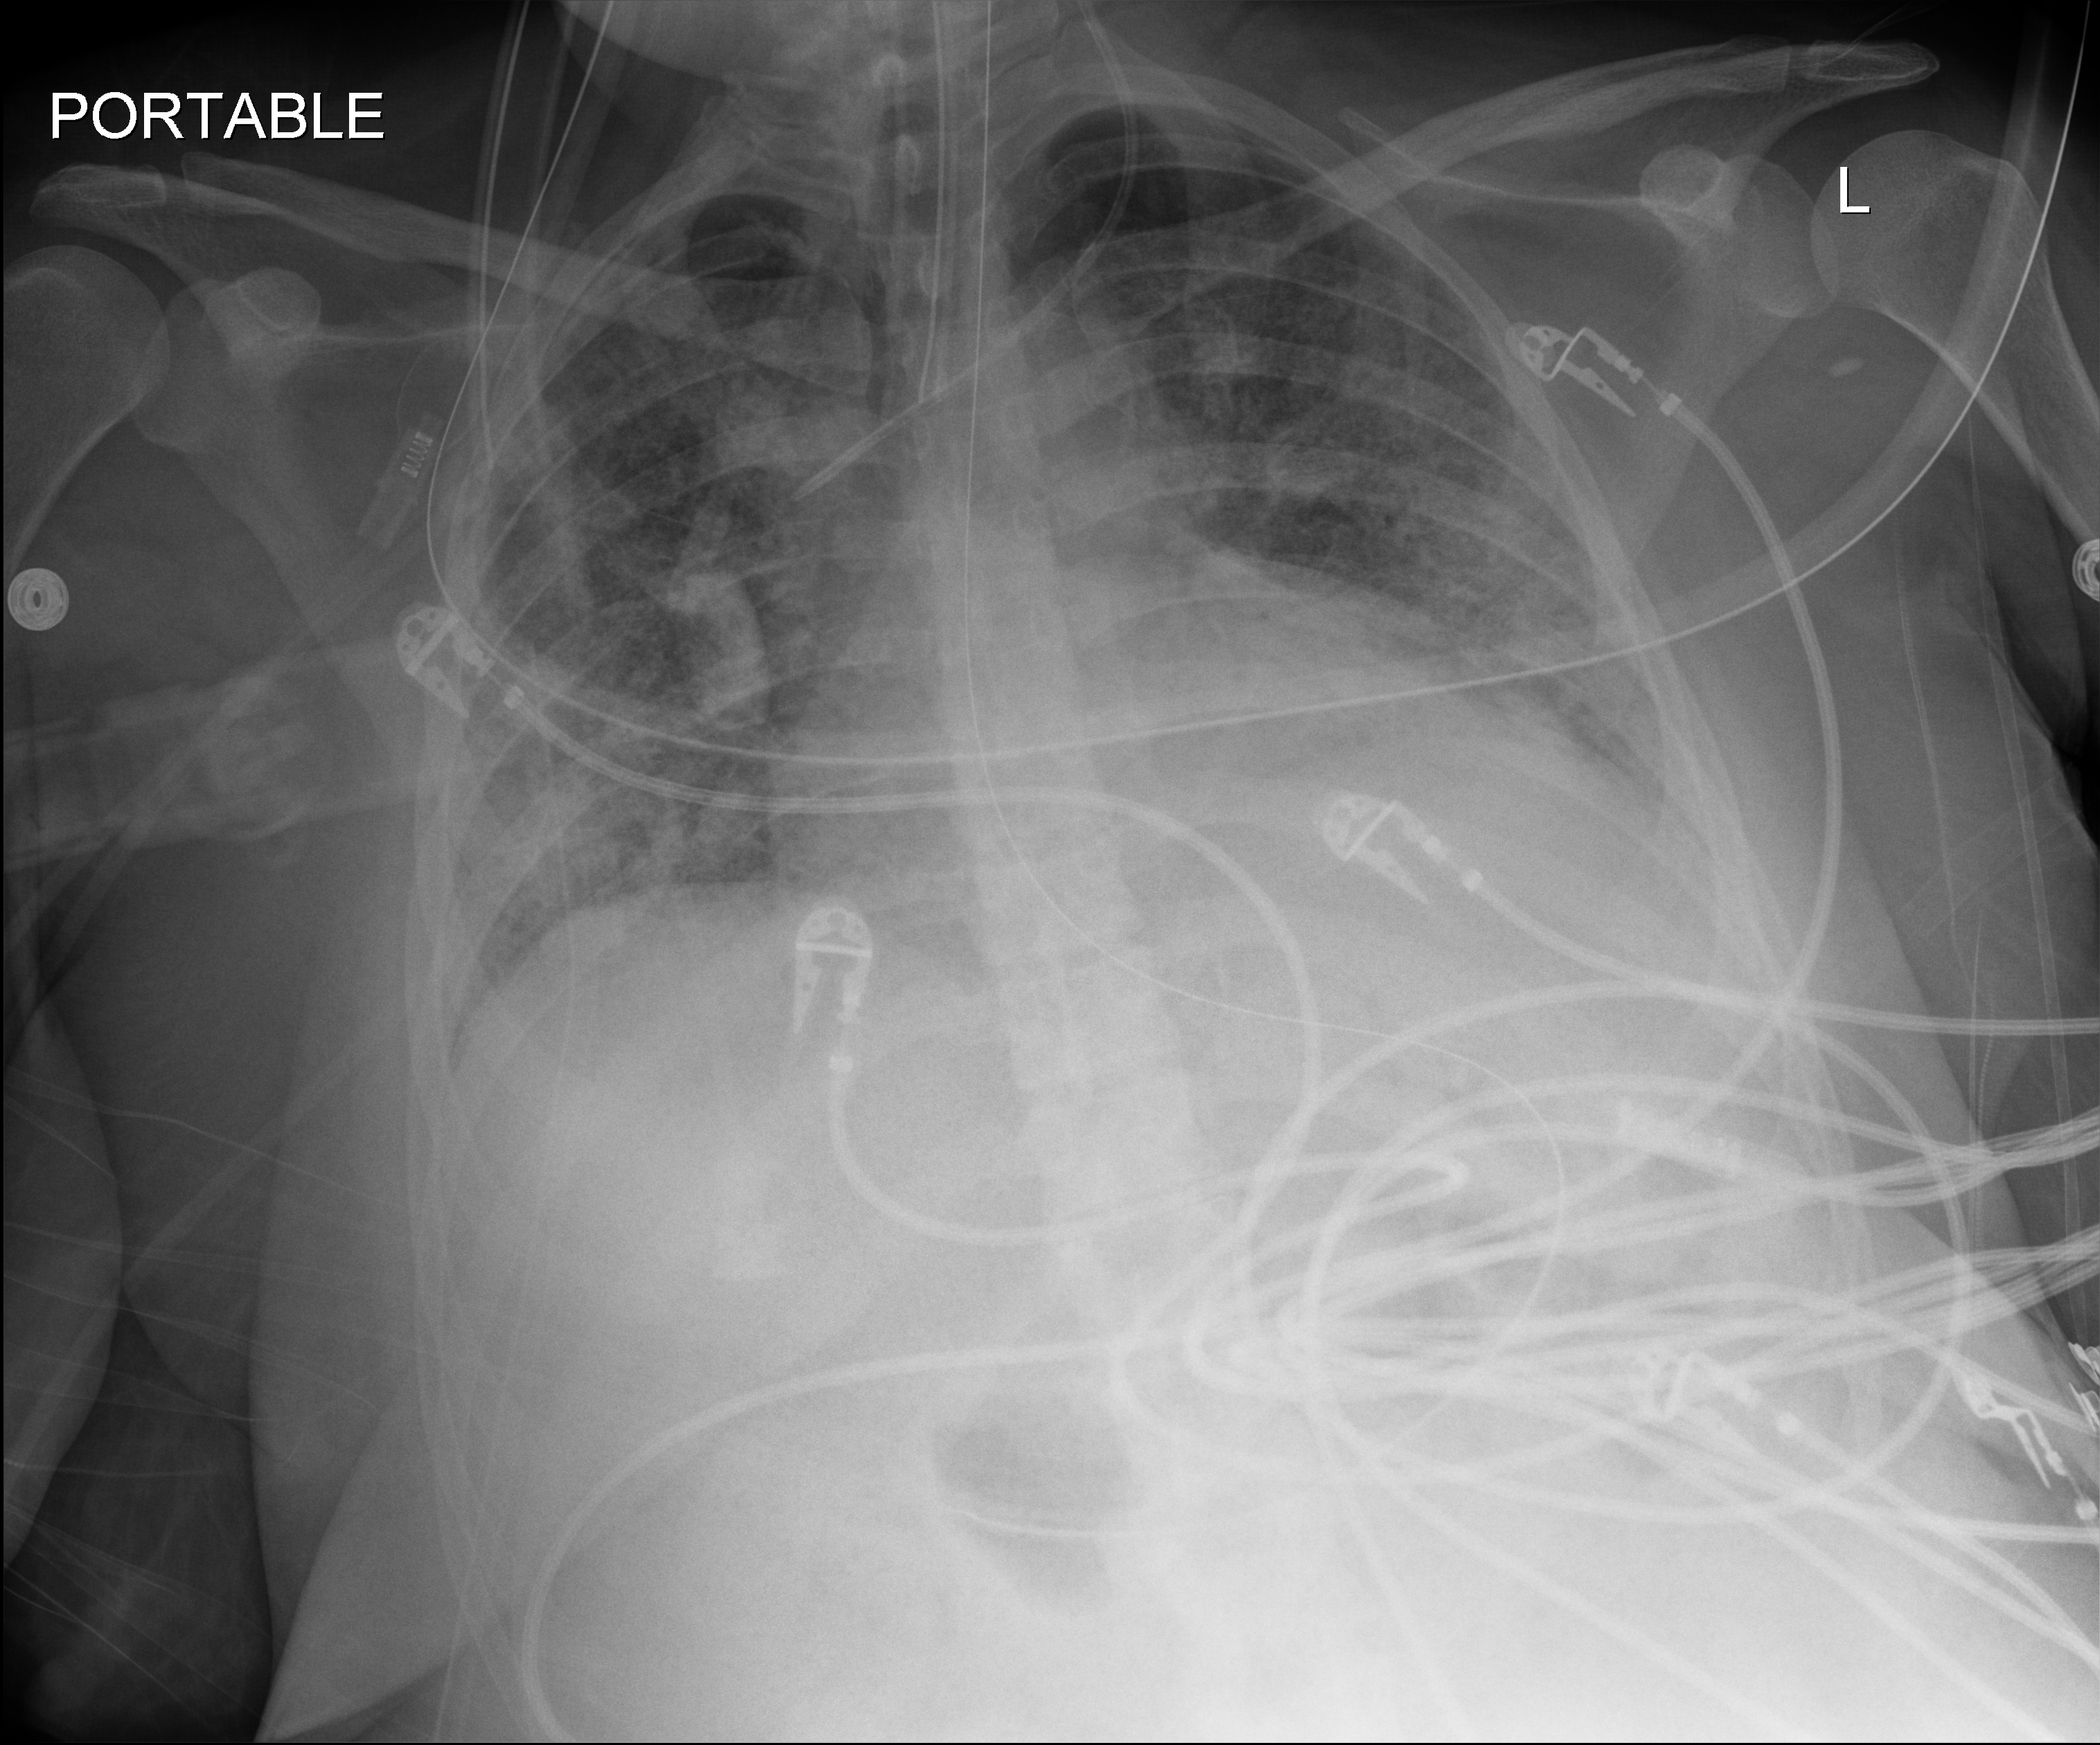
Portable chest radiograph; anteroposterior (AP) projection. Female patient hospitalised with COVID-19, age 18–59 years.
Admission-level facts for this patient (not findings on this image; timing relative to this image not recorded): admitted to intensive care during this hospital stay: no; mechanically ventilated during this hospital stay: yes.